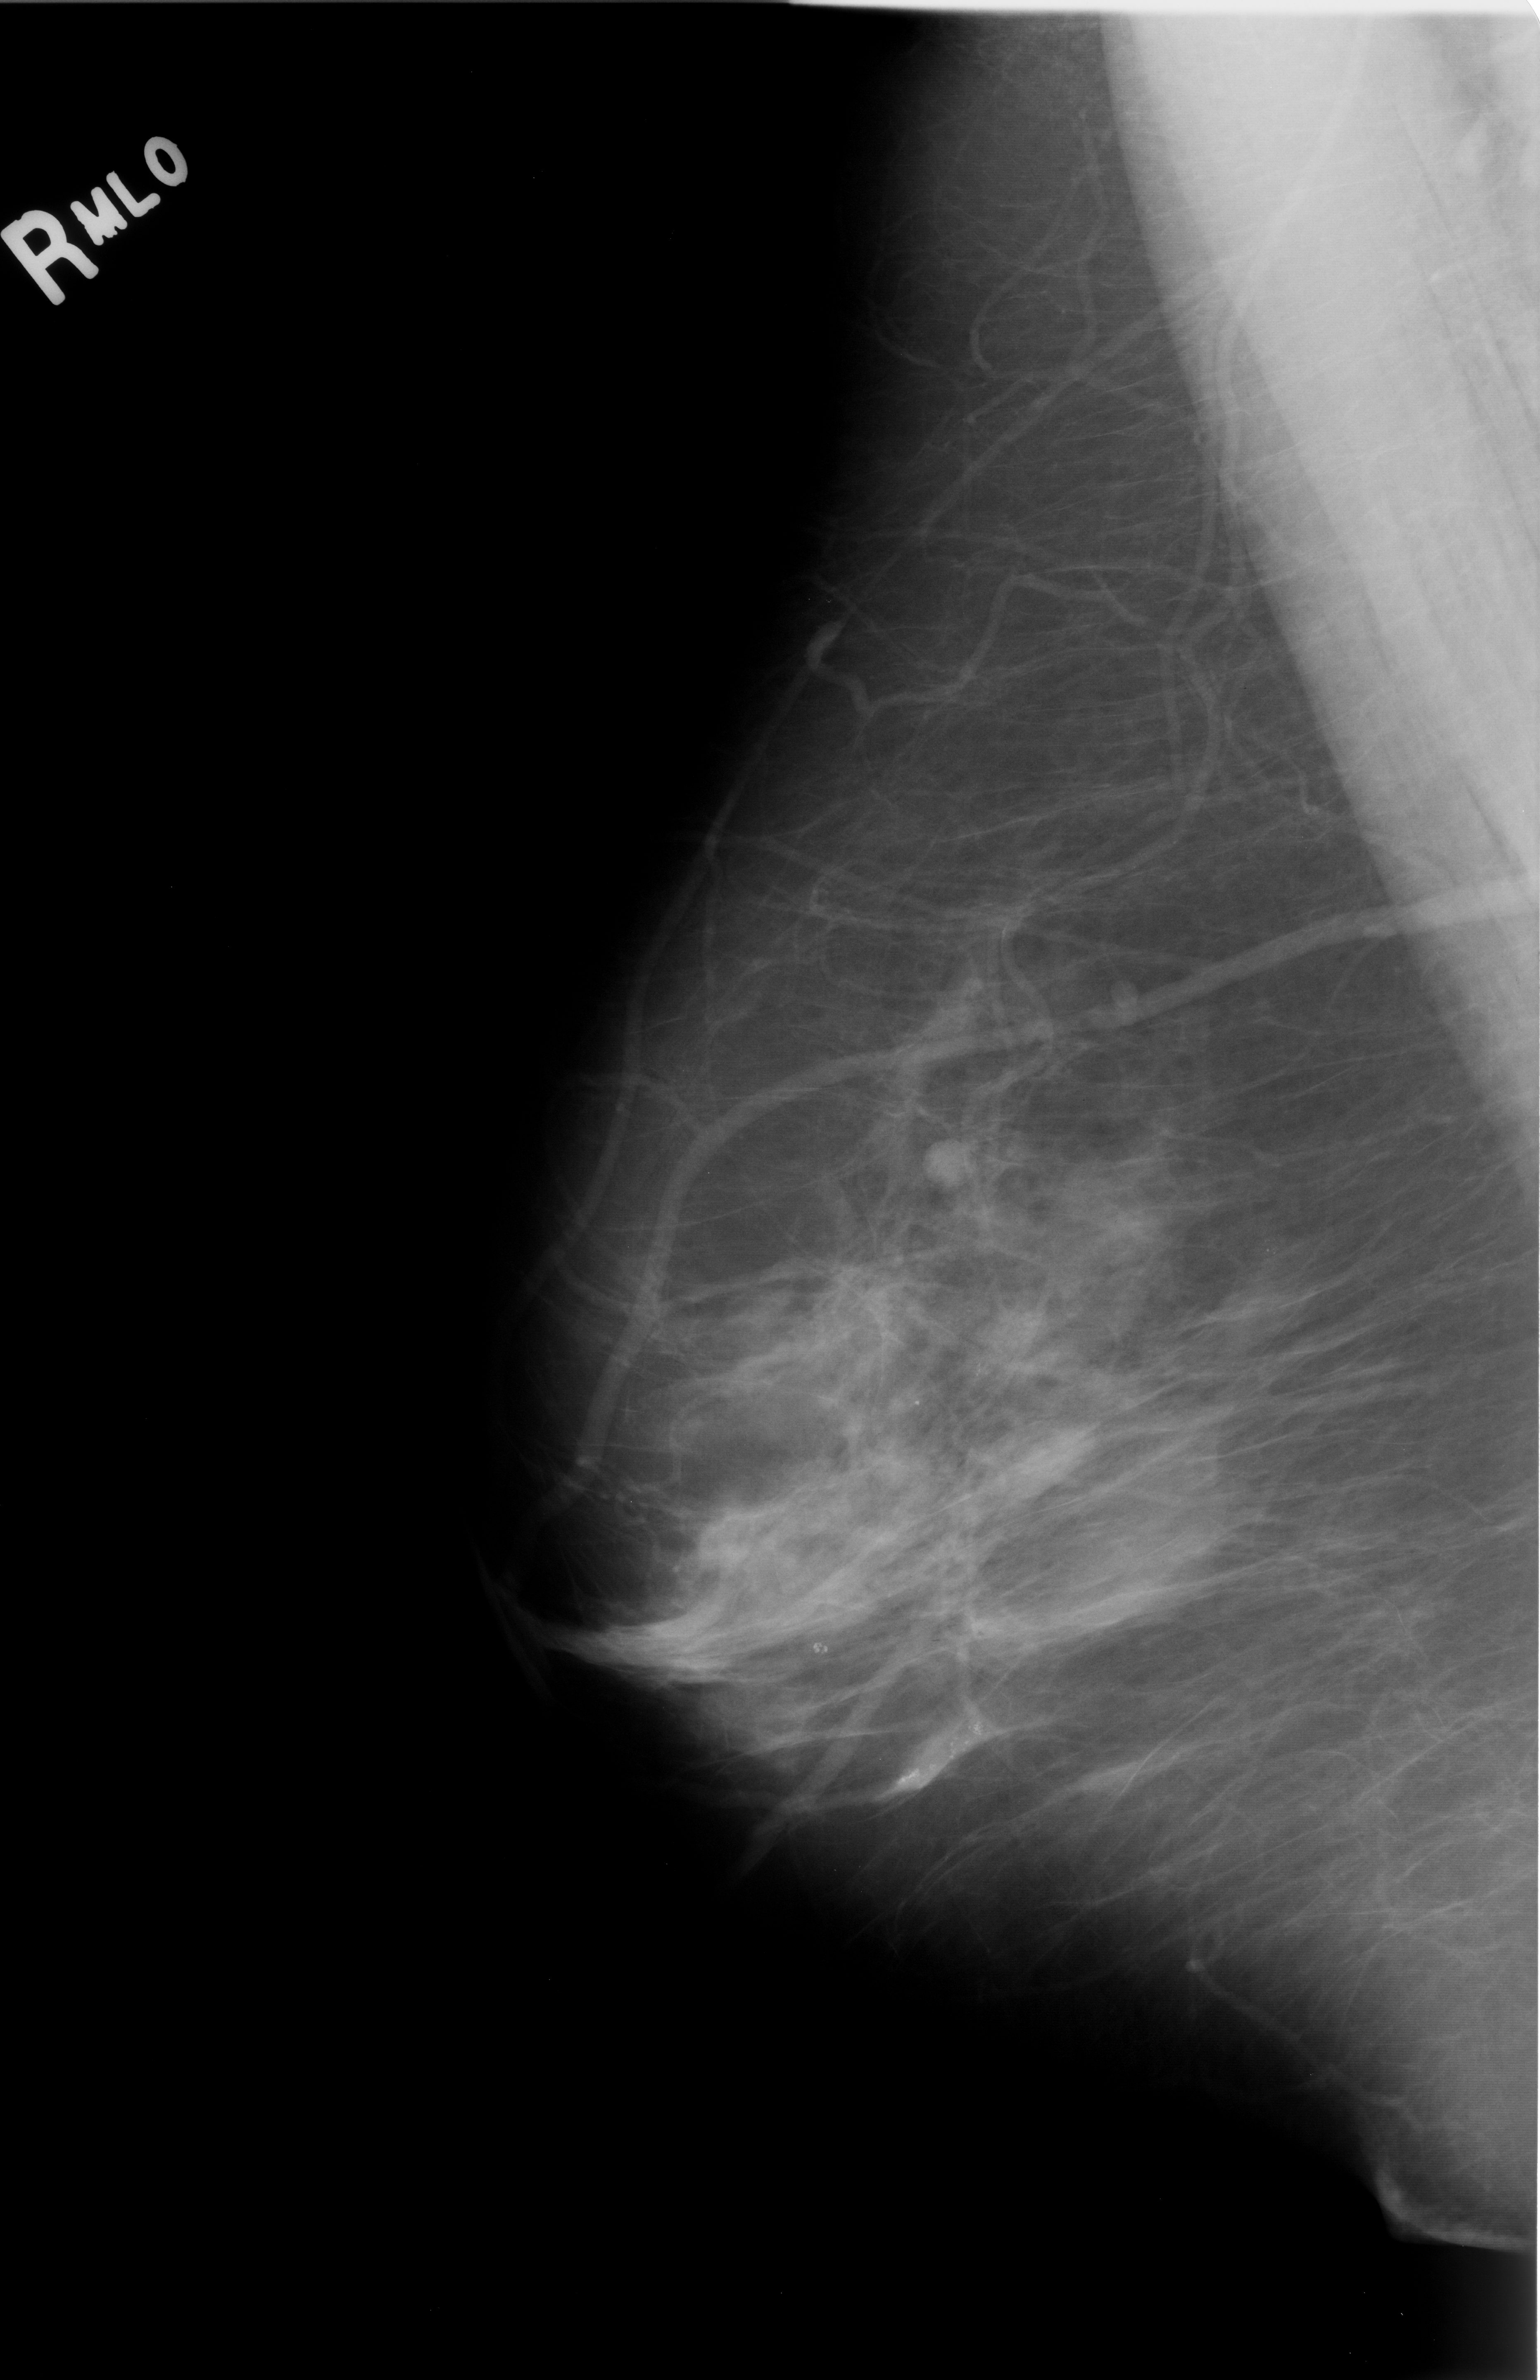
Digitized screen-film mammogram. Right breast. Mediolateral oblique (MLO) view. 1540 × 2380 image matrix.
Marked abnormalities (boxes around the expert regions of interest):
- Finding 1 of 2: calcifications, morphology pleomorphic, distribution clustered; BI-RADS assessment category 3; subtlety rating 5 on a 1 (subtle) to 5 (obvious) scale; pathology (as recorded): benign: bounding box <770,1586,880,1700> (left, top, right, bottom; pixels)
- Finding 2 of 2: calcifications, morphology pleomorphic, distribution clustered; BI-RADS assessment category 4; subtlety rating 5 on a 1 (subtle) to 5 (obvious) scale; pathology result (as recorded, not read from the image): benign: <852,1675,1029,1822>